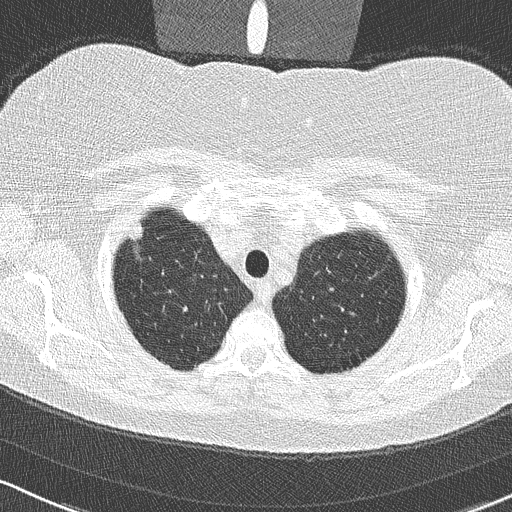
Axial slice from a low-dose chest CT screening exam; third screening round (two years after baseline); lung window (W 1500 / L -600 HU); 2 mm slice thickness; lung (sharp) reconstruction kernel (B50f); 120 kVp; slice 42 of 315 in the series. Female, age 58 years at enrolment. Former smoker at enrolment.
Expert-annotated lung lesion, bounding box [x1, y1, x2, y2] px = [117, 219, 158, 262]. The screening reader recorded 2 non-calcified nodules or masses ≥4 mm on this exam (right upper lobe, right lower lobe); which of them this box marks is not recorded. Later outcome: lung cancer diagnosed 48 days after this screen — bronchiolo-alveolar adenocarcinoma, NOS, right upper lobe, well differentiated (G1), stage IA (AJCC 6th edition), 9 mm at pathology.